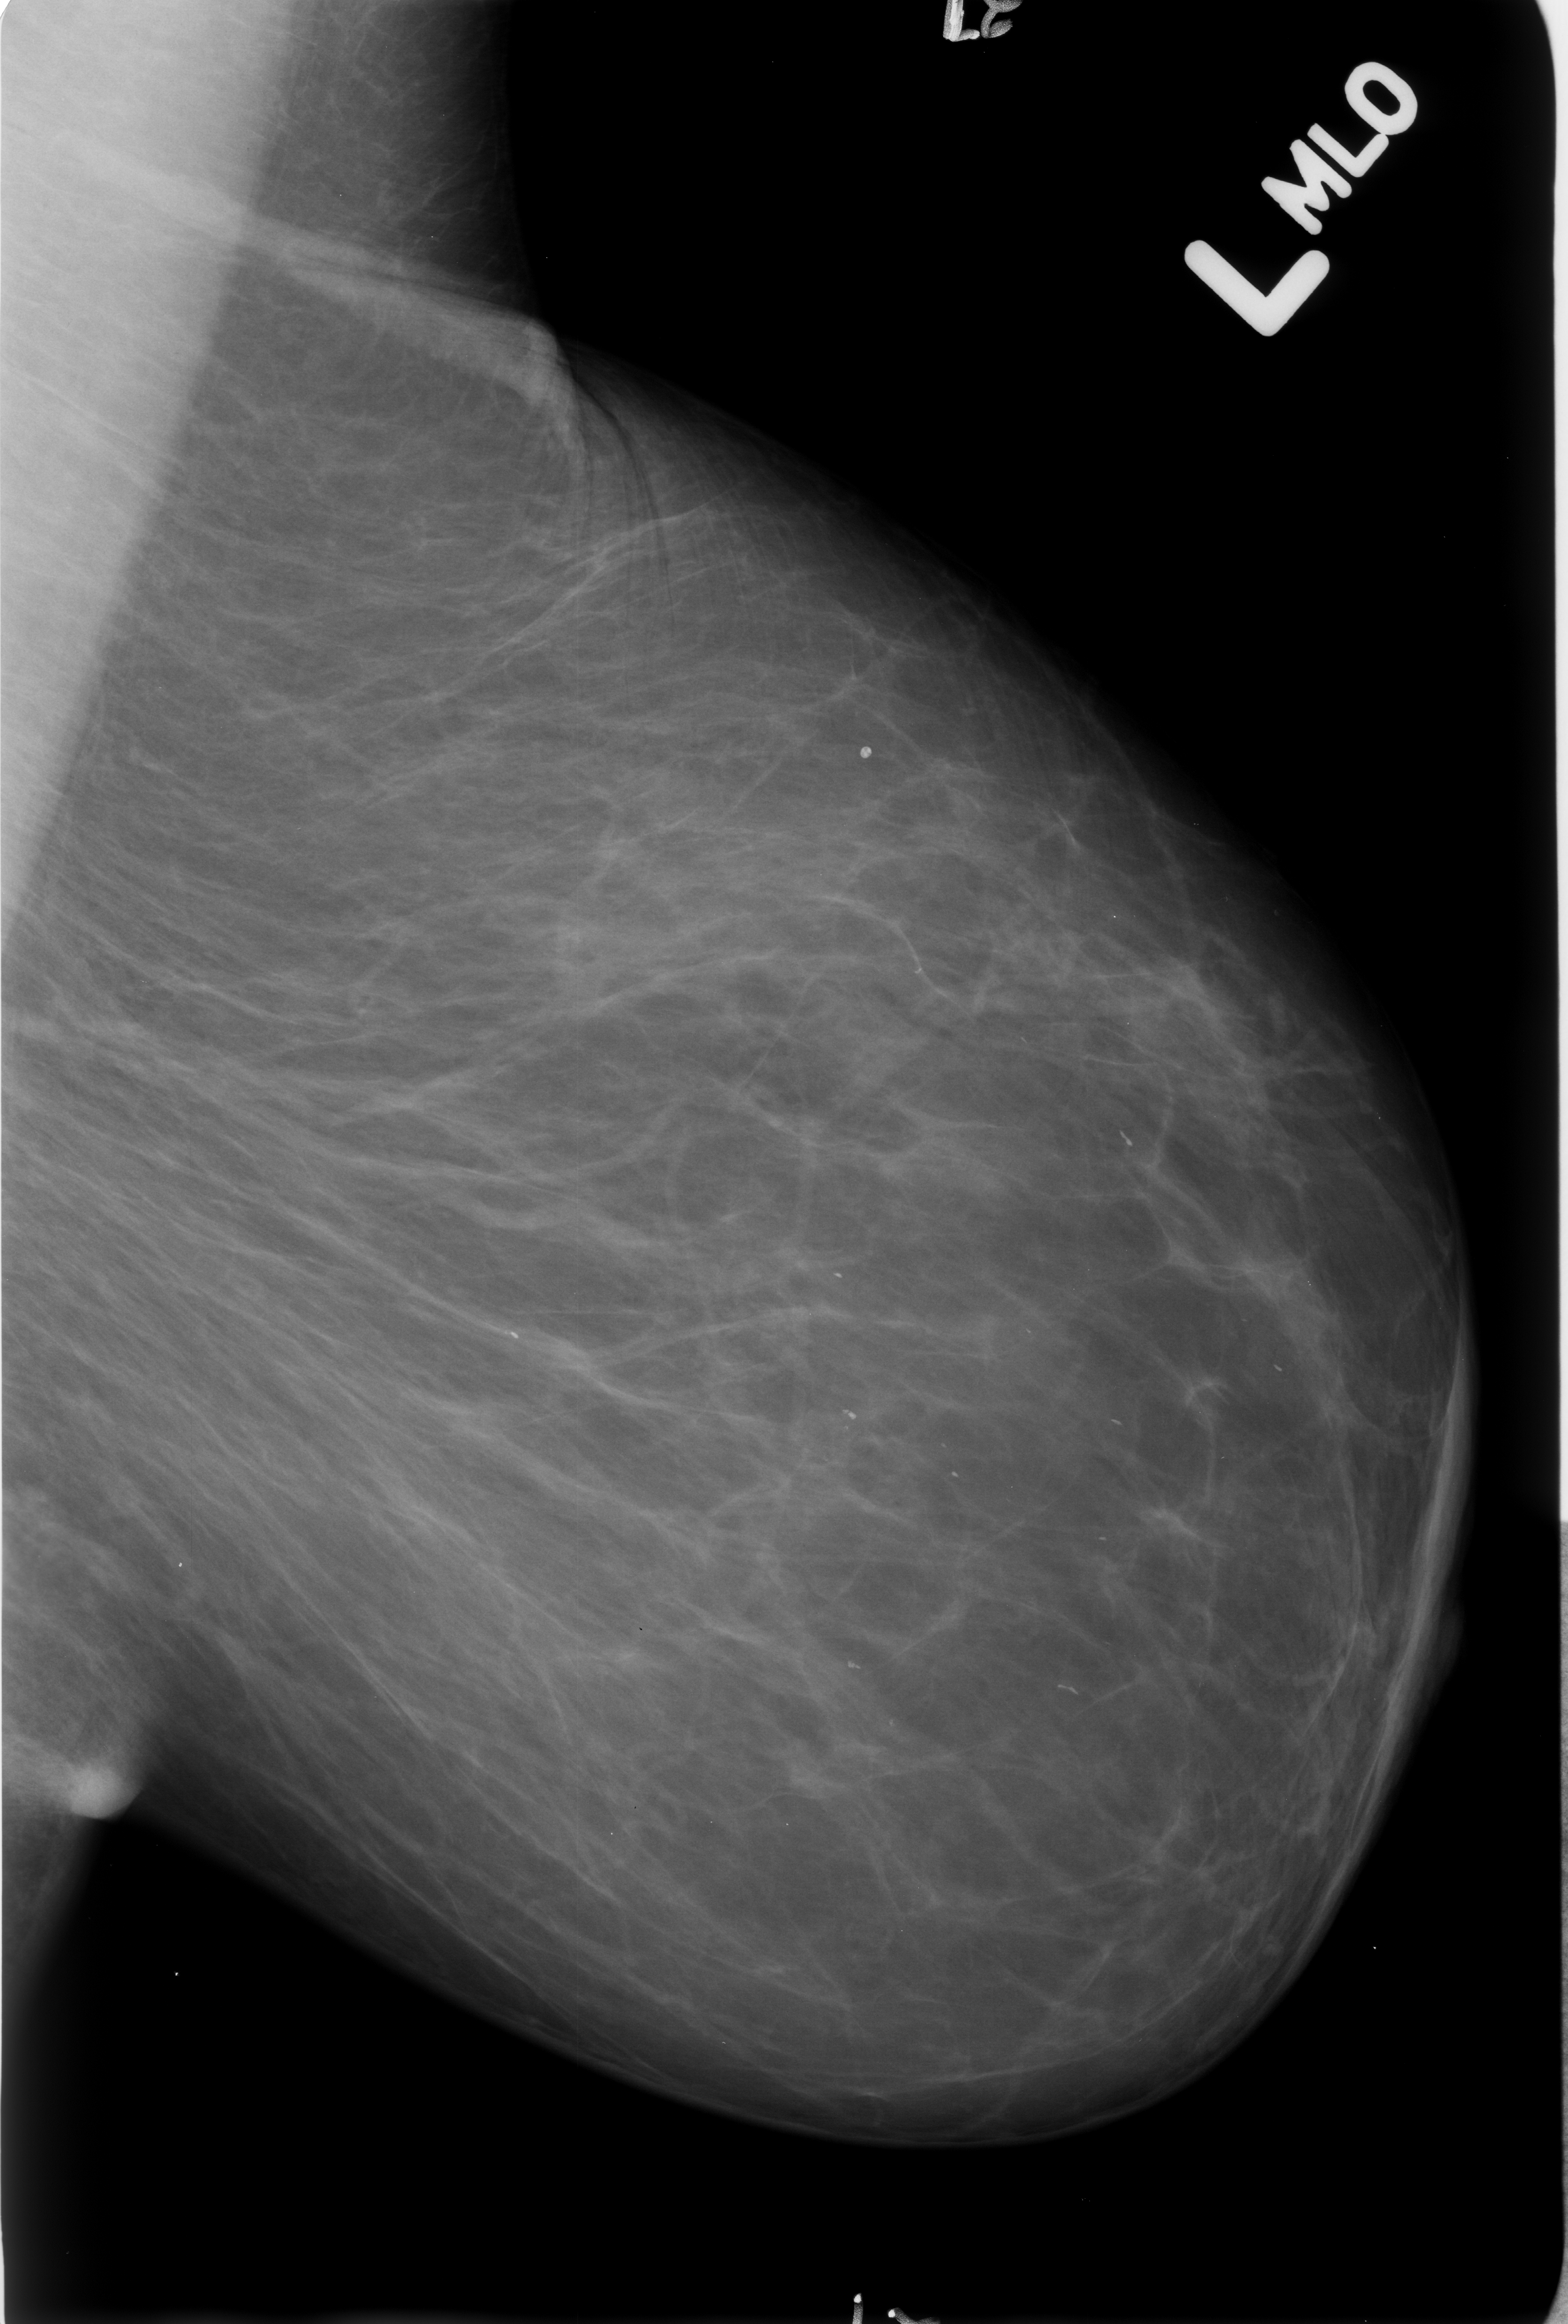
Digitized screen-film mammogram. Left breast. Mediolateral oblique (MLO) view. Breast composition: almost entirely fatty (BI-RADS density category 1 of 4). 1568 × 2324 image matrix.
Marked abnormalities (boxes around the expert regions of interest):
- Finding 1 of 3: calcifications, distribution regional; BI-RADS assessment category 2; subtlety rating 3 on a 1 (subtle) to 5 (obvious) scale; outcome (as recorded, no biopsy): benign without callback (not worked up further): box from (x=1046, y=1671) to (x=1101, y=1713) px
- Finding 2 of 3: calcifications, distribution regional; BI-RADS assessment category 2; subtlety rating 3 on a 1 (subtle) to 5 (obvious) scale; outcome (as recorded, no biopsy): benign without callback (not worked up further): (x=1095, y=1396)–(x=1142, y=1450)
- Finding 3 of 3: calcifications, distribution regional; BI-RADS assessment category 2; benign; no additional work-up was recommended (outcome (as recorded, no biopsy): benign without callback): (x=1108, y=1116)–(x=1159, y=1163)